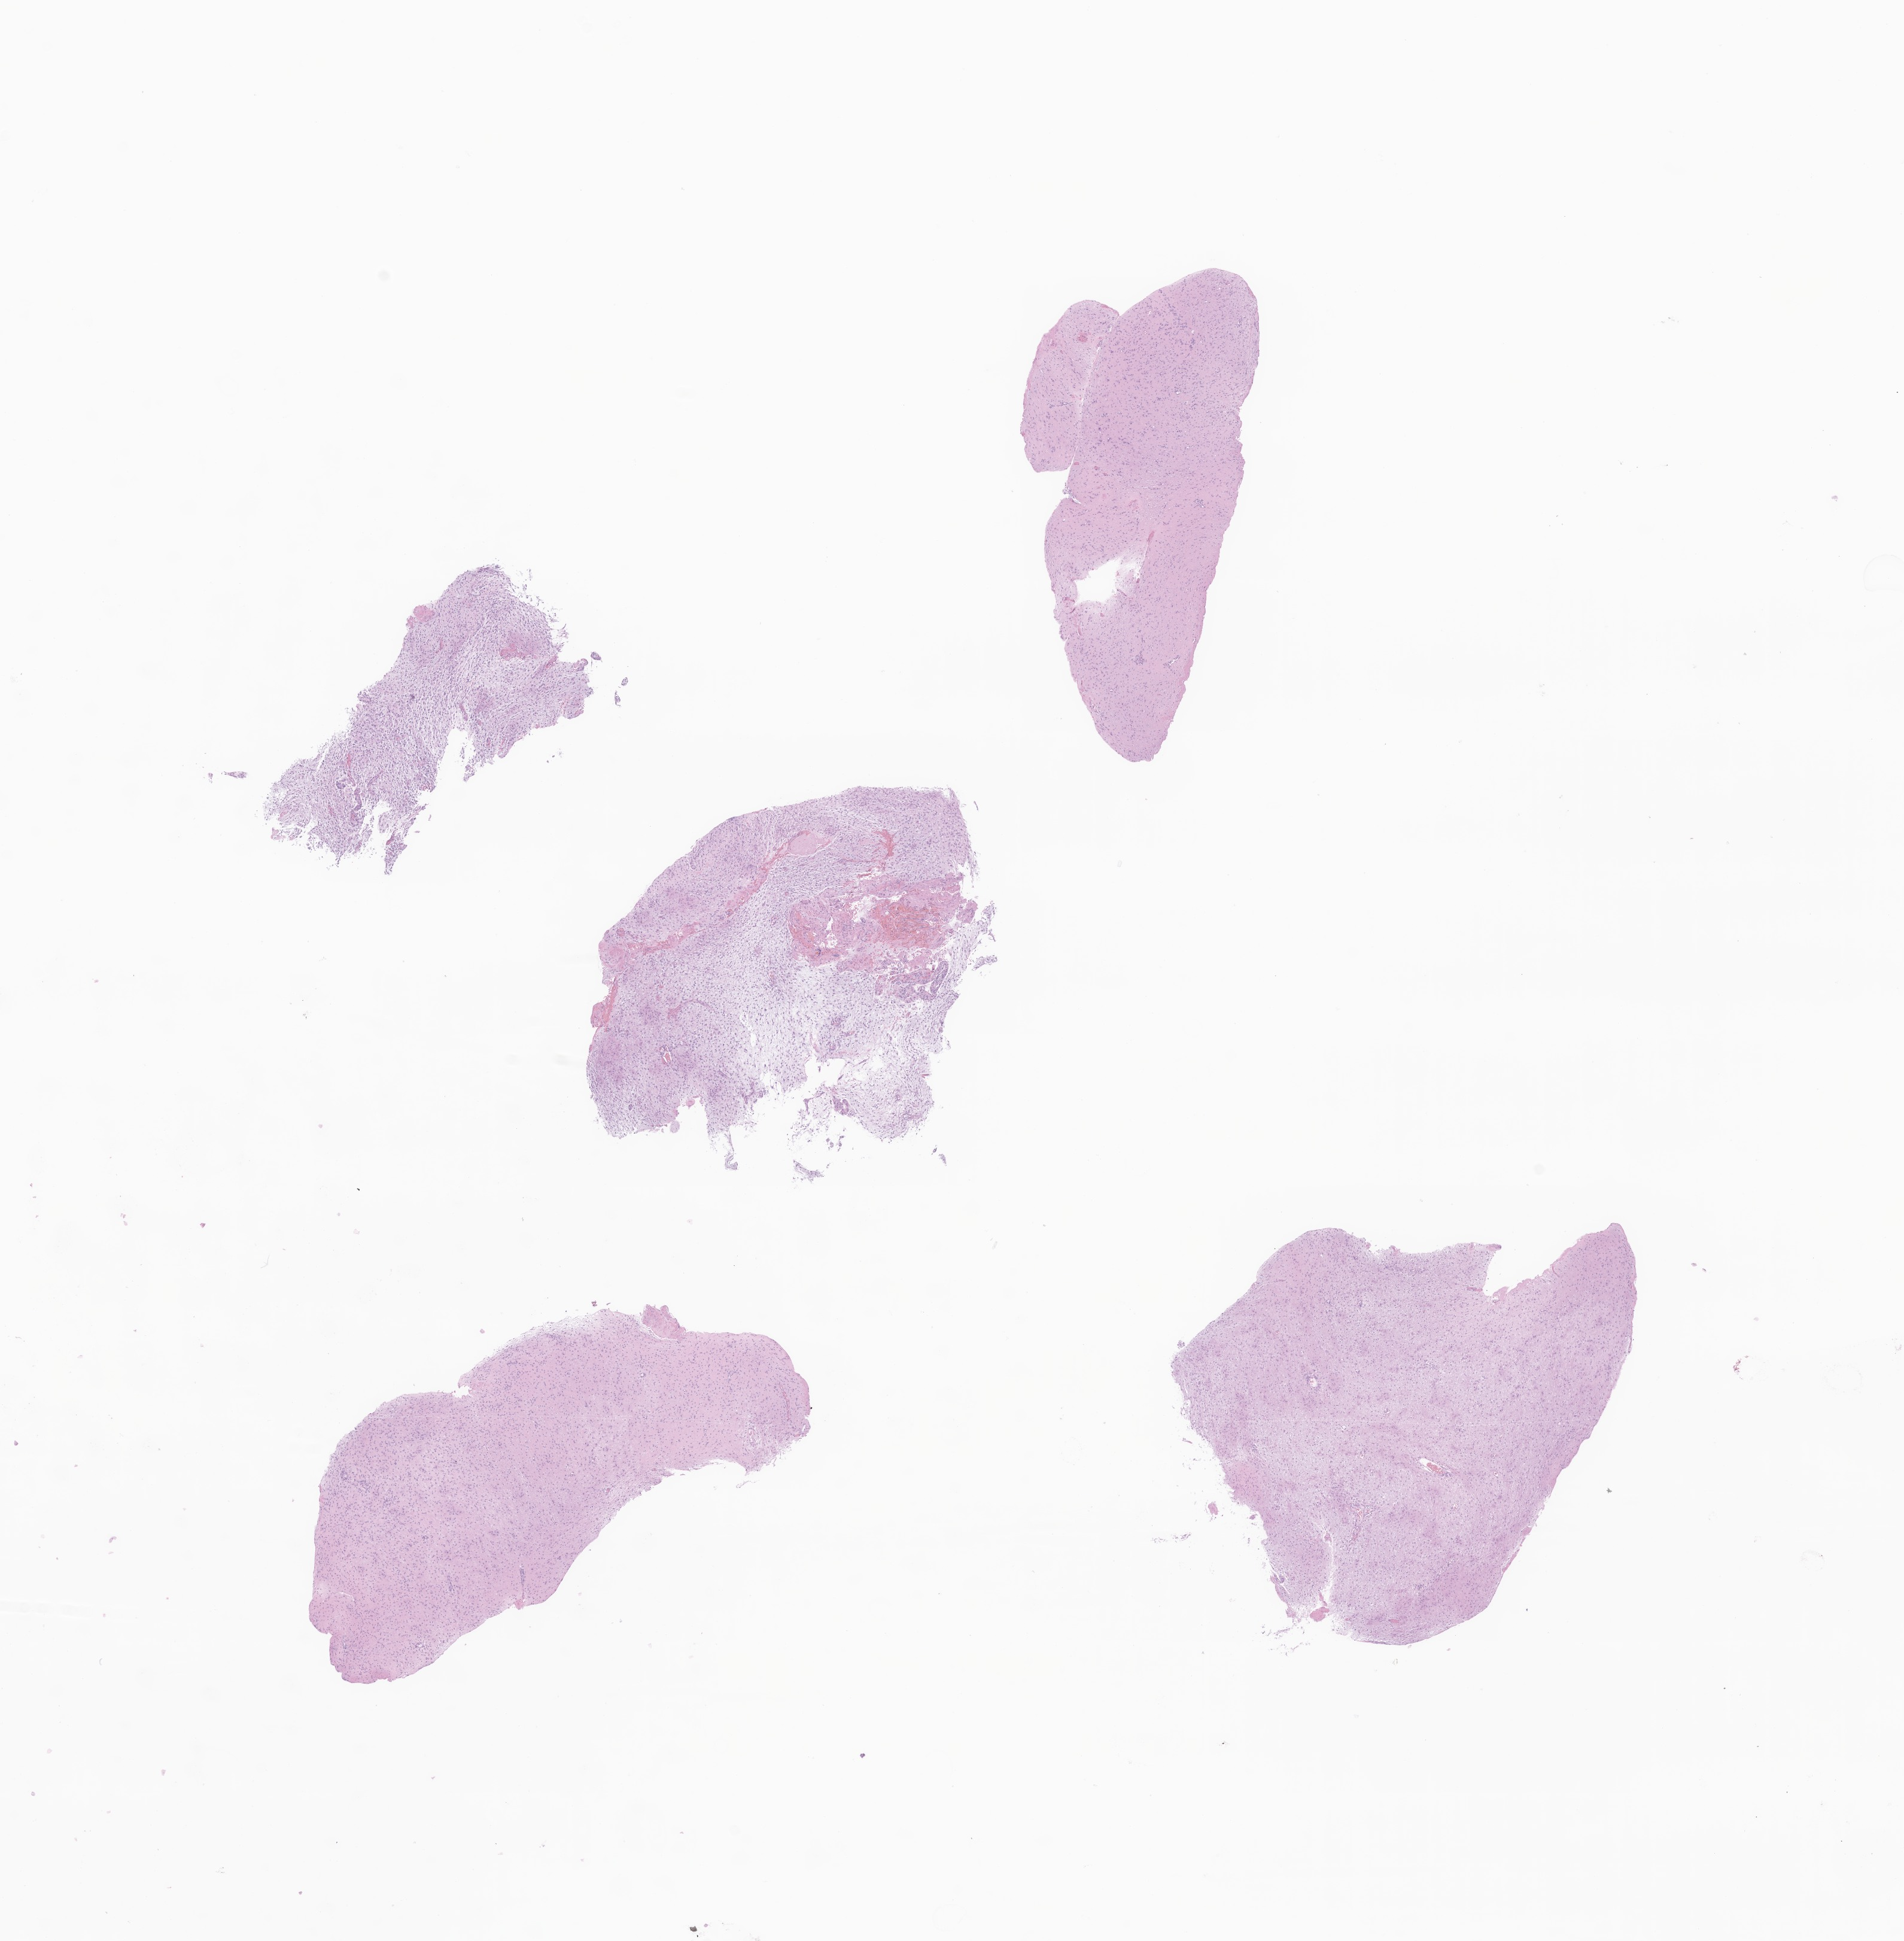
Hematoxylin and eosin (H&E) whole-slide image of tumor tissue from the brain stem — a low-resolution overview of the entire scanned area, about 13.4 x 13.7 mm, formalin-fixed paraffin-embedded section. Patient female; age 599 days (about 1.6 years).
• diagnosis (ICD-O-3 morphology term): Pilocytic astrocytoma